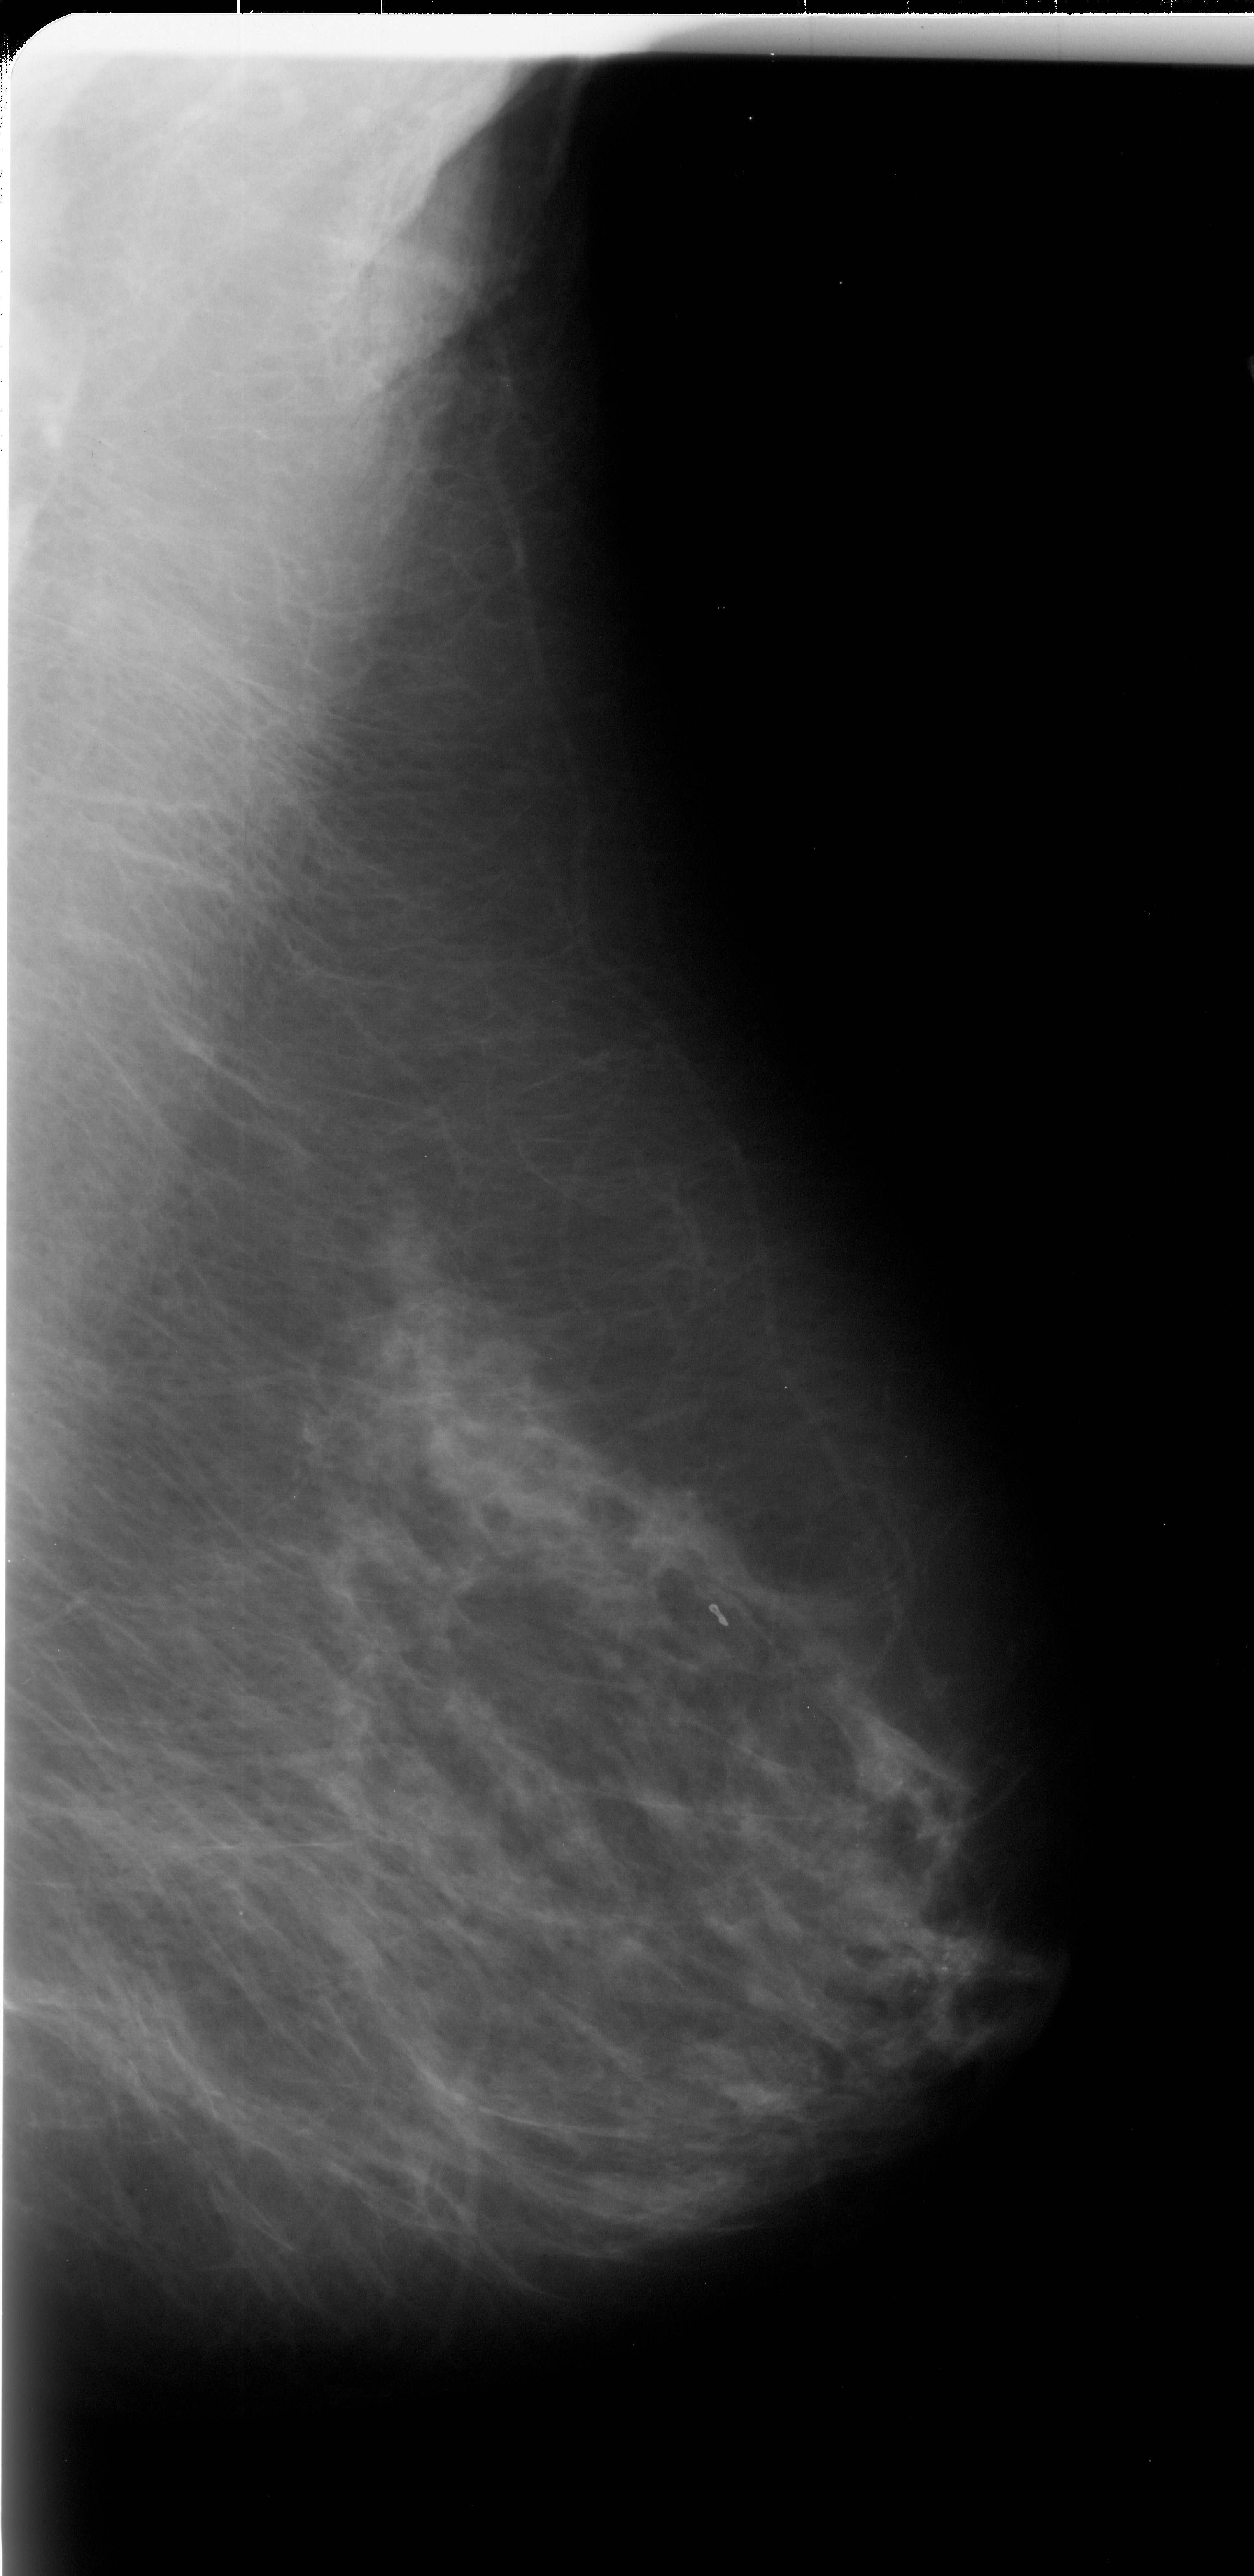
Mammogram (digitized film); right breast; mediolateral oblique (MLO) view; BI-RADS breast density category 2 (scale 1–4); 1254 × 2576 image matrix.
Marked abnormalities (boxes around the expert regions of interest):
- calcifications, morphology fine linear branching, distribution linear; BI-RADS assessment category 5; subtlety rating 4 on a 1 (subtle) to 5 (obvious) scale; pathology (as recorded): malignant: box from (x=822, y=1722) to (x=1047, y=2021) px